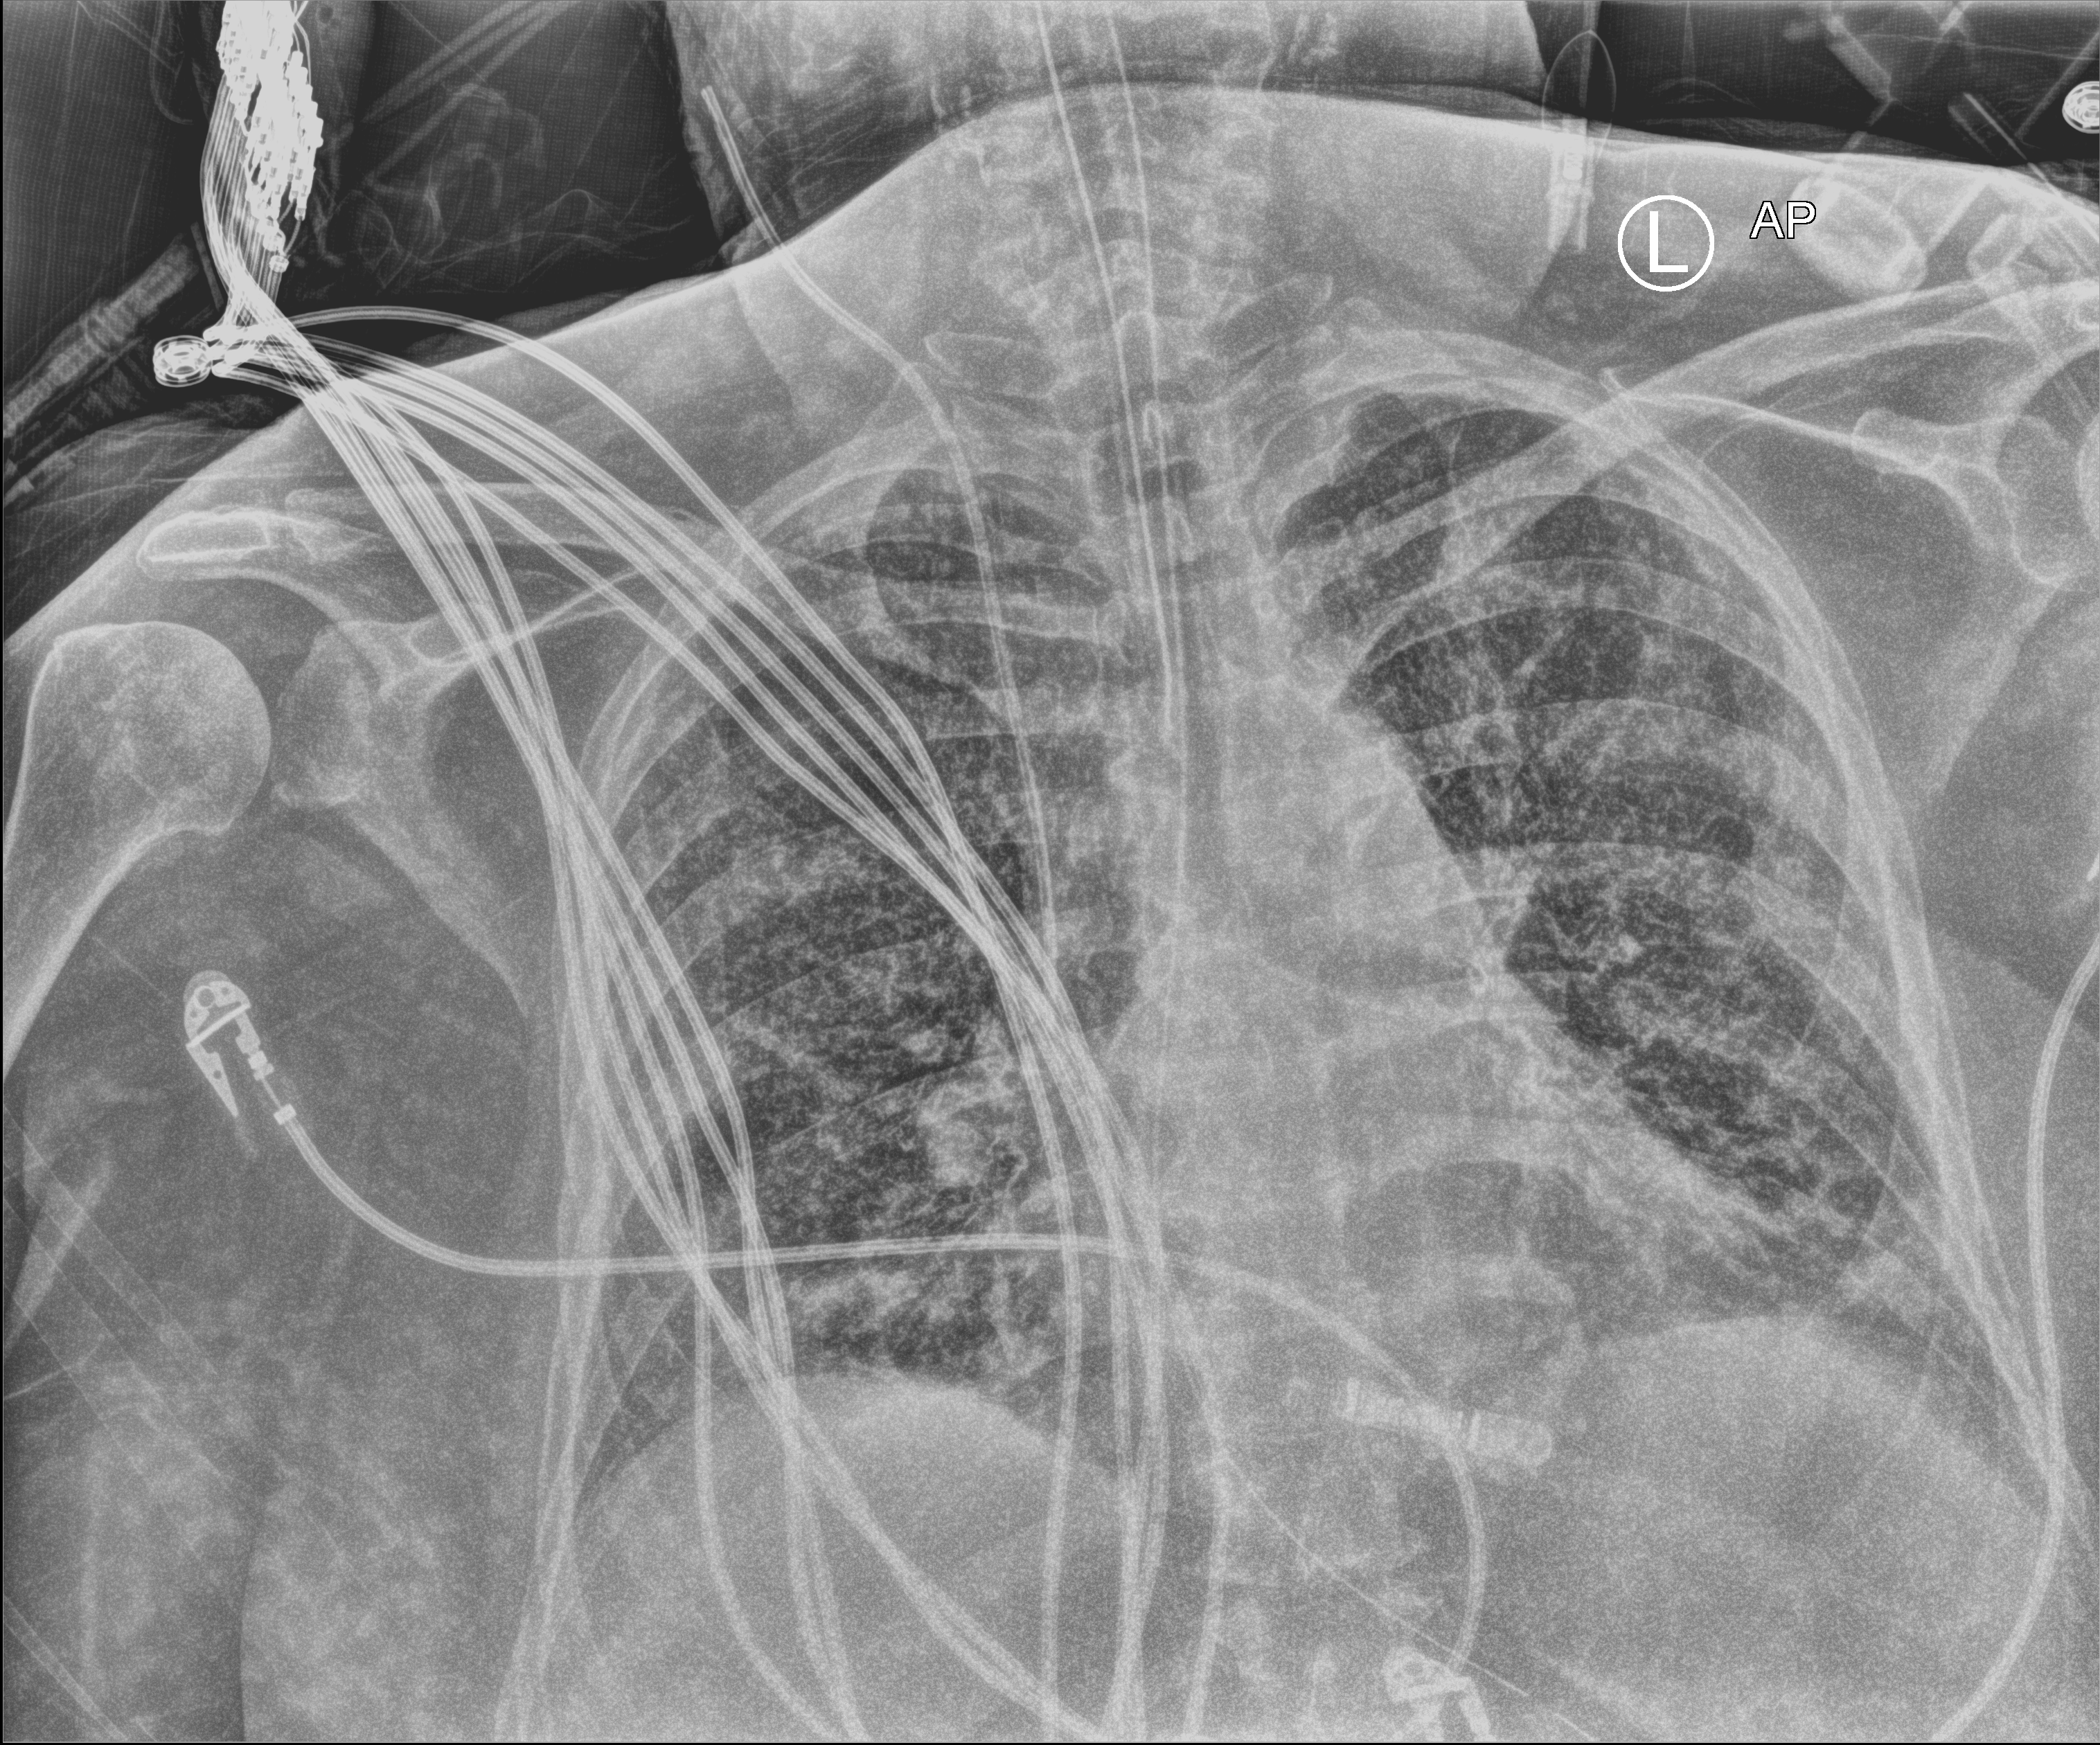
Bedside chest radiograph (computed radiography); anteroposterior (AP) projection. Patient hospitalised with COVID-19; female, aged 60–74 years.
From the hospital-stay record, not from the radiograph (when in the stay this image was taken is not recorded):
- mechanically ventilated during this hospital stay: yes
- length of hospital stay: 28 days
- admitted to intensive care during this hospital stay: yes